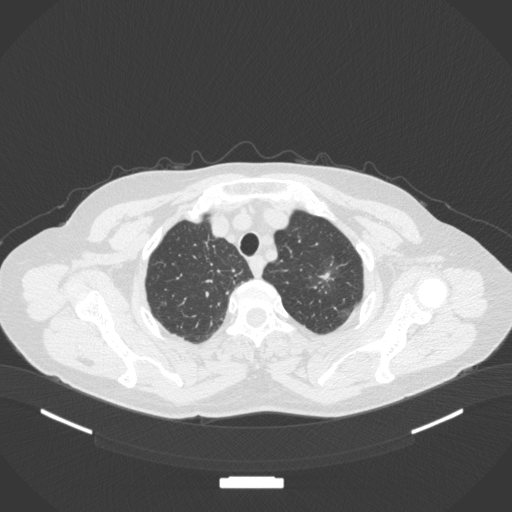
Chest CT, one axial slice; slice 310 of 369 in the series (ordered by position); reconstruction kernel B31f; 120 kVp; lung window (W 1500 / L -600 HU); 1 mm slice thickness; 512 × 512 image matrix. Female patient, age 64 years. Case-level facts recorded for this patient, not image findings: clinical TNM (as recorded): T1c N0 M0.
Structures marked on this image (bounding box drawn by a radiologist):
- lung tumour (recorded histology: adenocarcinoma): bounding box [x1, y1, x2, y2] px = [305, 251, 348, 298]